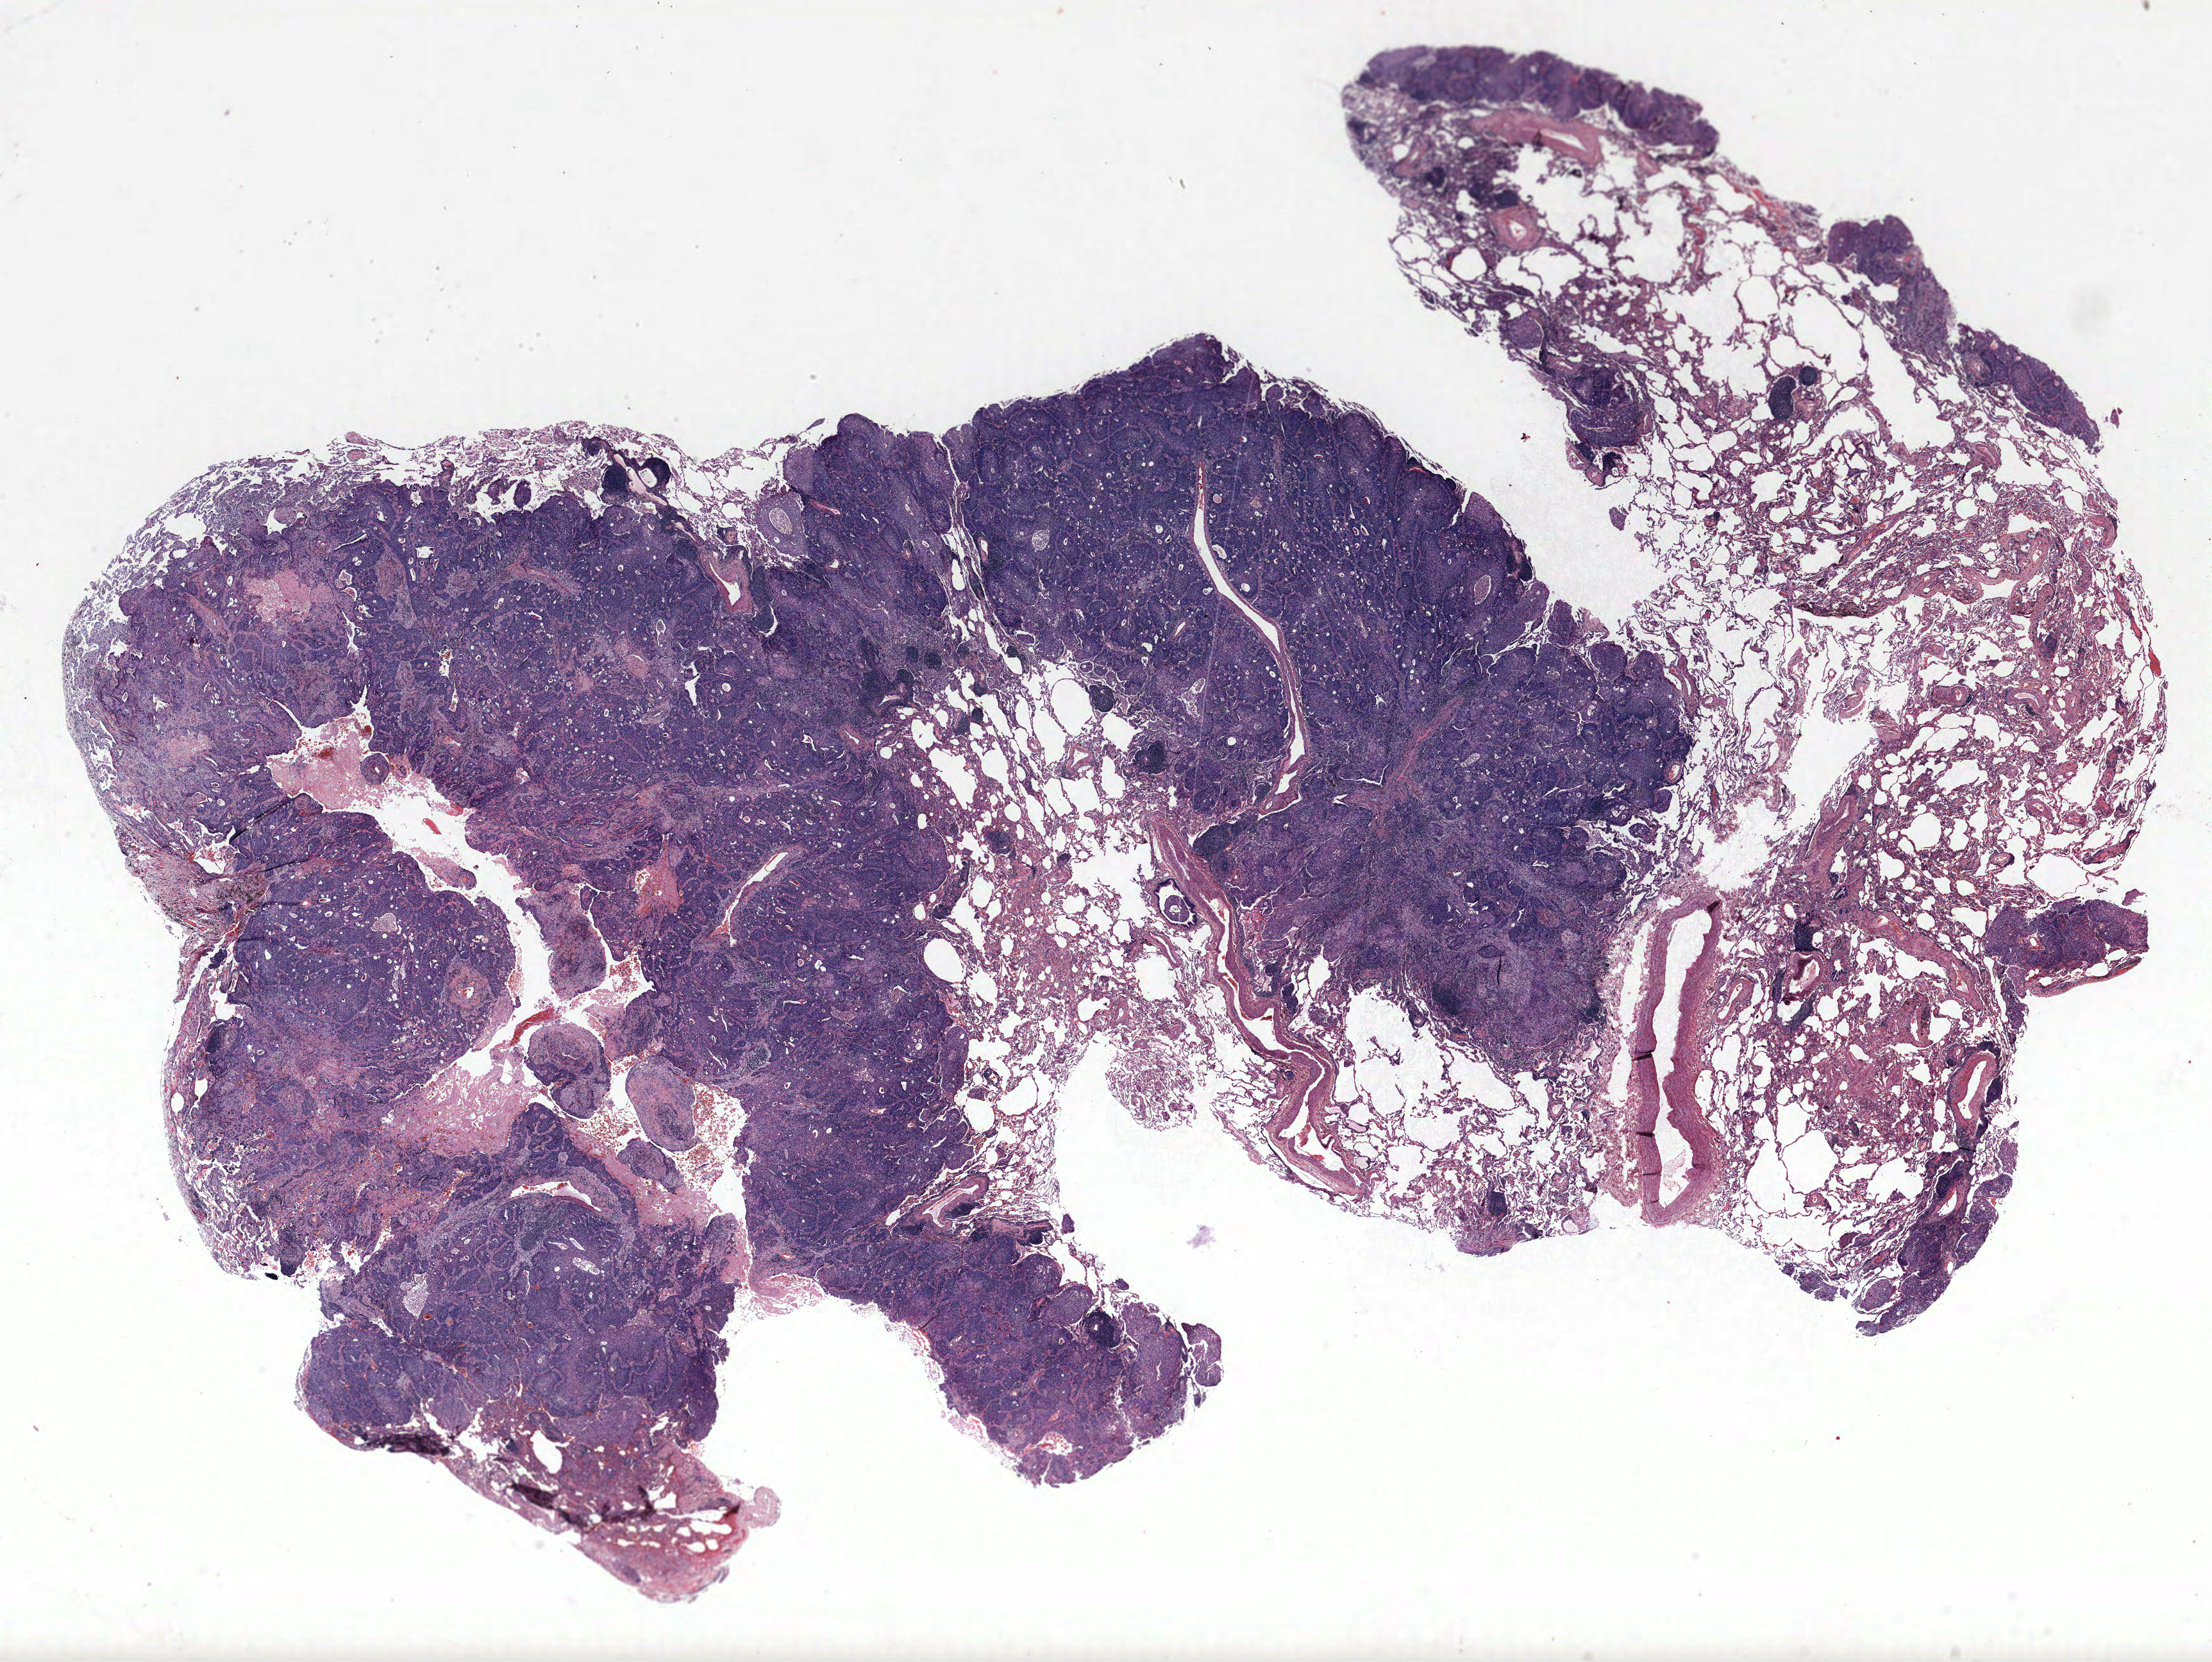
Whole-slide histology image, H&E — a low-resolution overview of the entire scanned area, about 27.6 x 20.7 mm; FFPE section; lung tissue. Male, age 67 at enrolment. Former smoker at enrolment.
Participant's lung-cancer diagnosis: Squamous cell carcinoma, NOS (ICD-O-3 8070/3).